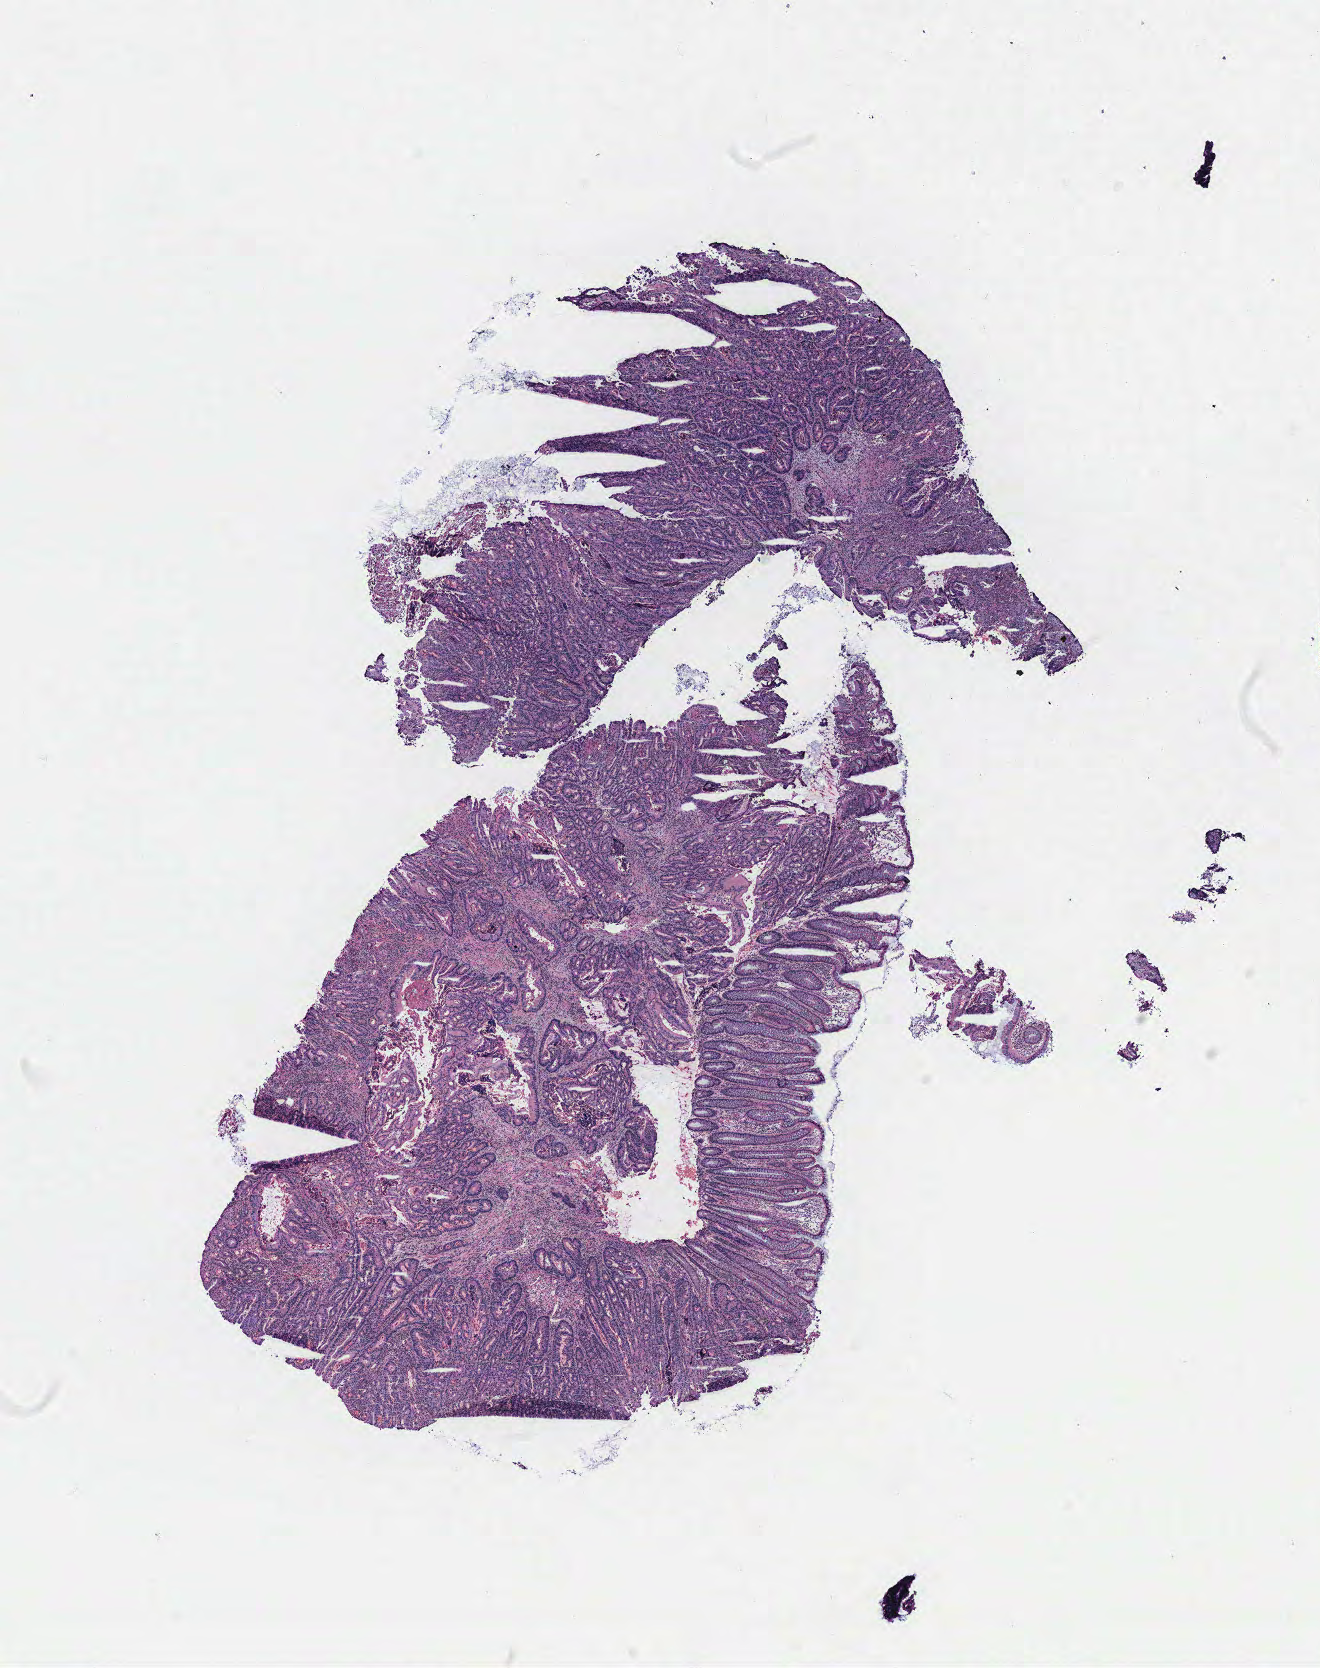
Digitized Hematoxylin and eosin (H&E) stained tissue section (whole slide), shown as a low-resolution overview of the whole scanned area (about 10.6 x 13.3 mm). Colon, tissue type not recorded.
- patient diagnosis (cohort enrolment): colon cancer (colon)